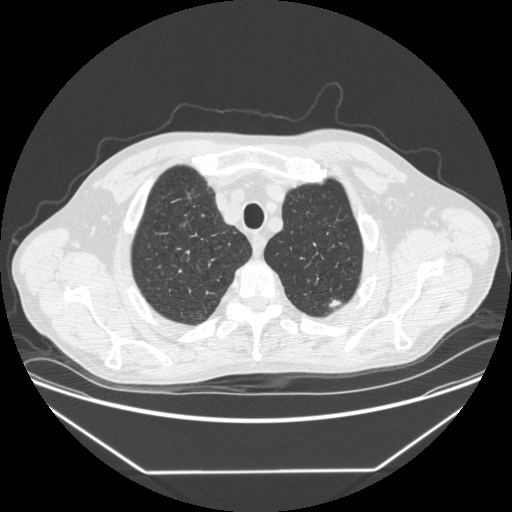
Low-dose screening chest CT, one axial slice. Slice 336 of 383 in the series (ordered by position). Reconstruction kernel STANDARD. Lung window (W 1500 / L -600 HU). 1.25 mm slice thickness. 512 × 512 image matrix.
Annotated regions visible in this slice (outlined manually by an expert reader):
- lesion 1 (tumor, upper lobe of left lung): bounding box (x1, y1, x2, y2) in pixels: (329, 300, 342, 311)